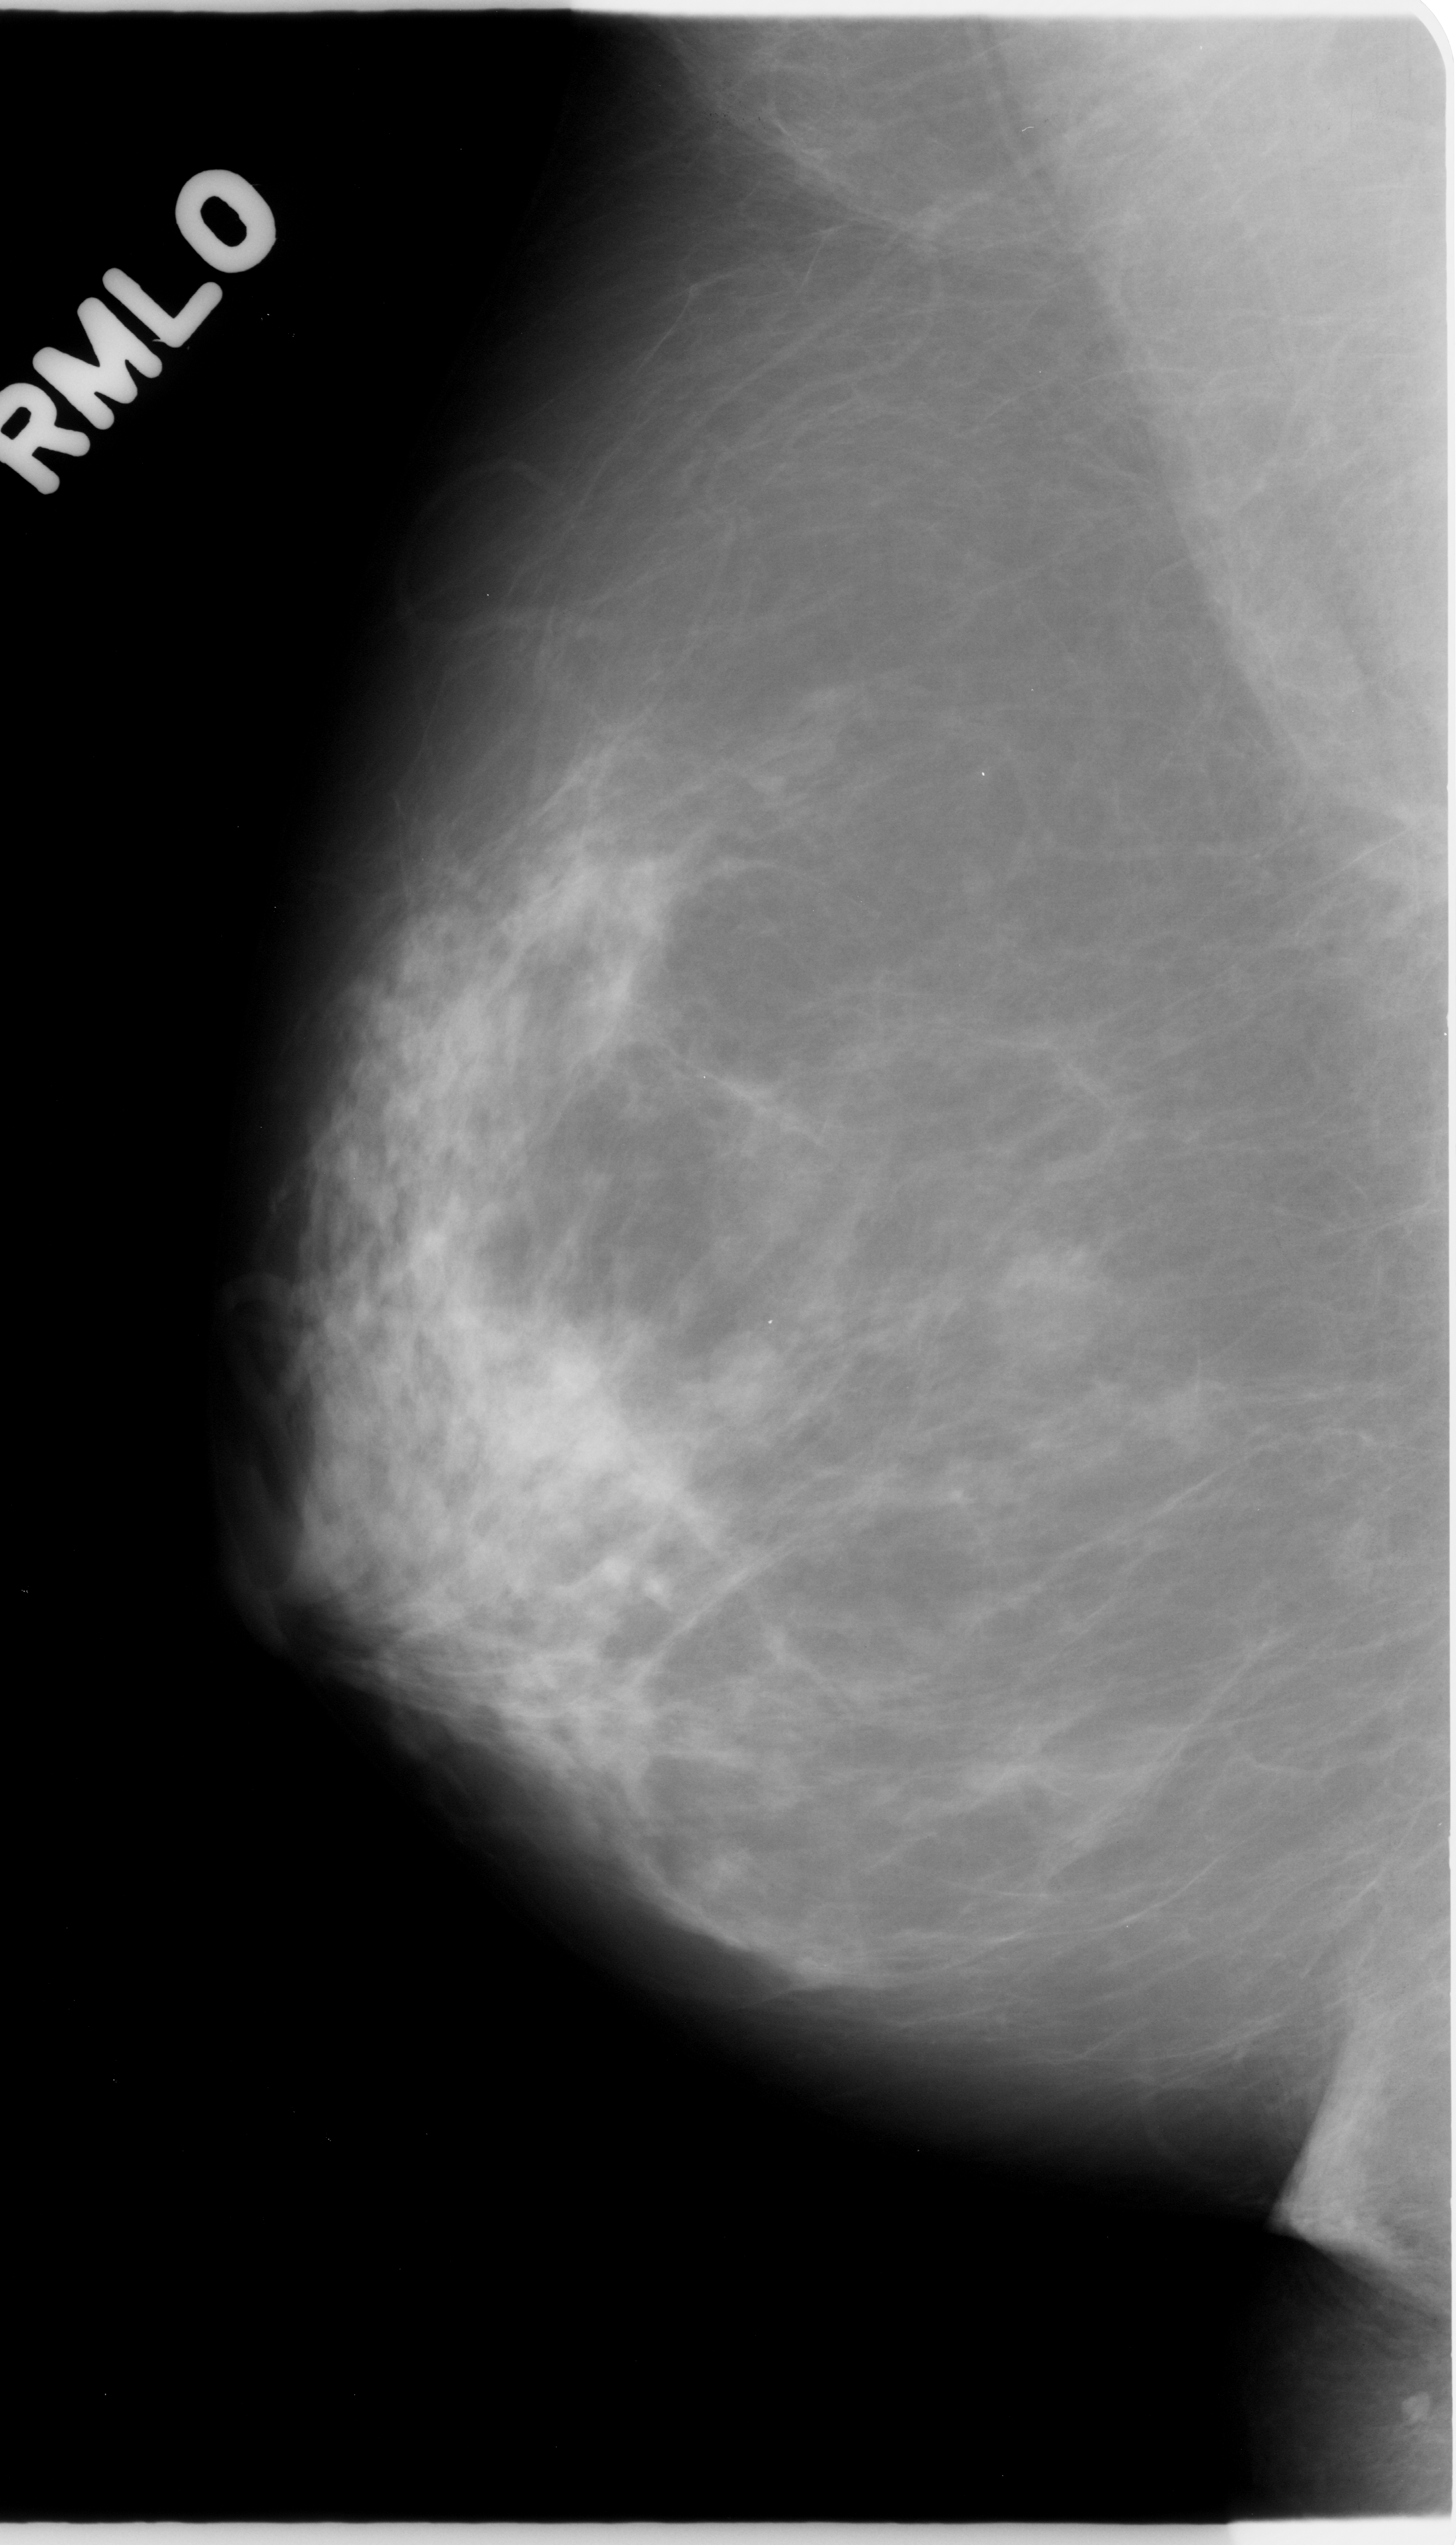
Digitized screen-film mammogram, right breast, MLO view, breast composition: scattered fibroglandular densities (BI-RADS density category 2 of 4).
- Mass, shape oval, margins circumscribed; BI-RADS assessment category 3; subtlety rating 5 on a 1 (subtle) to 5 (obvious) scale; pathology (as recorded): benign.